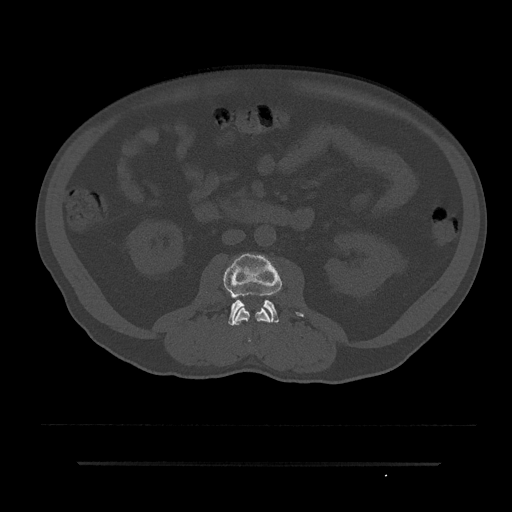
CT including the spine, one axial slice; position 33 of 797 along the scan axis; reconstruction kernel Br40s/3; bone window (W 1800 / L 400 HU); 0.5 mm slice thickness; 512 × 512 image matrix, field of view 464 × 464 mm. Patient: male, 59 years. Case-level facts recorded for this patient, not image findings: primary cancer: bile ducts; vertebrae with lytic lesions (as recorded): T10.
Structures marked on this image (semi-automatically segmented with operator editing):
- L2 vertebra: bounding box [x1, y1, x2, y2] px = [233, 303, 272, 343]
- L3 vertebra: [224, 254, 303, 325]